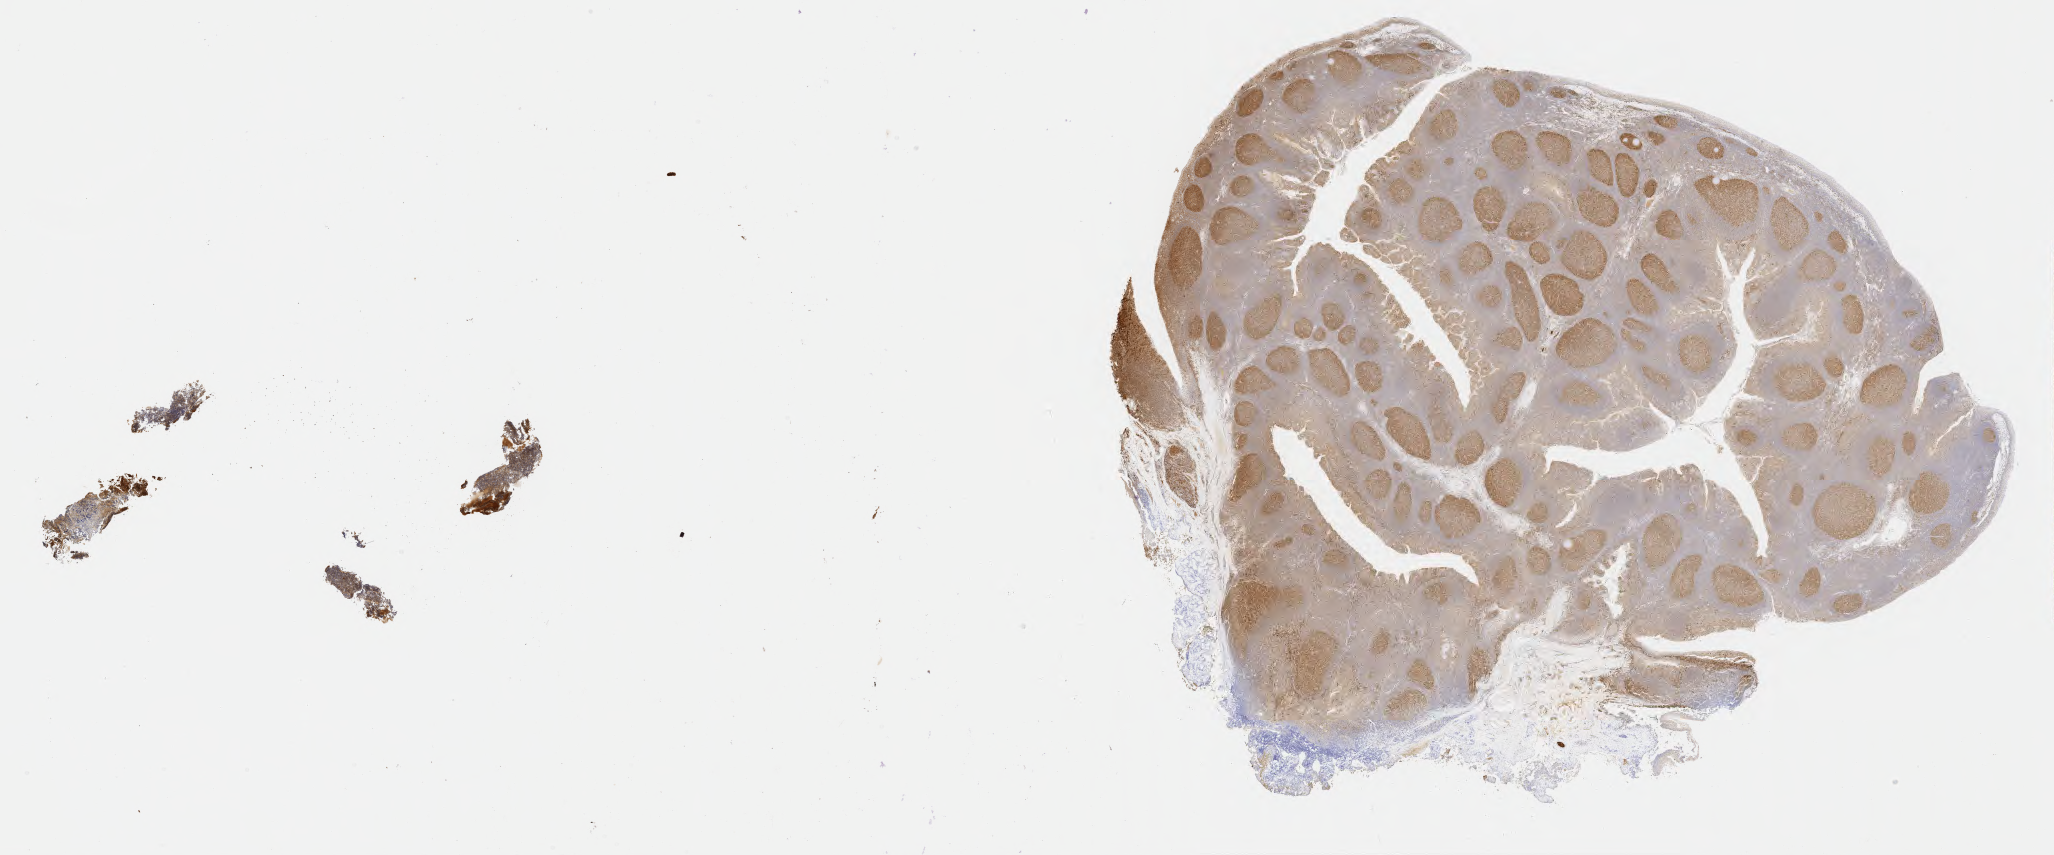
Immunohistochemistry (IHC) whole-slide image stained for BCL6 — low-resolution overview of the scanned area, about 33.2 x 13.8 mm; tumor tissue; anatomic site: lymph node of head and neck. Patient: female, age at initial diagnosis 4 years.
• diagnosis: Burkitt lymphoma, NOS